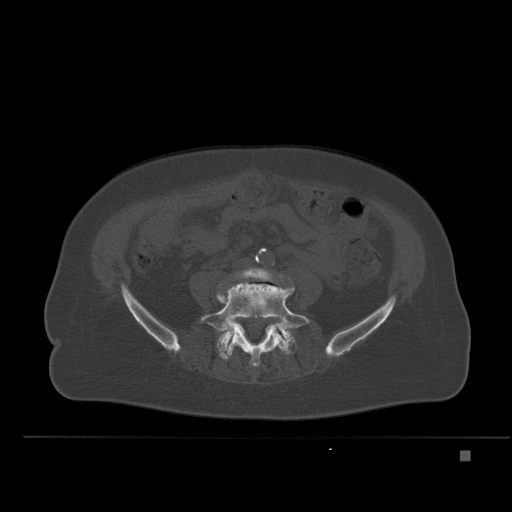
CT including the spine, one axial slice. Position 163 of 477 along the scan axis. Bone window (W 1800 / L 400 HU). 512 × 512 image matrix, field of view 422 × 422 mm. Female patient, age 74 years. Case-level facts recorded for this patient, not image findings: primary cancer: colon.
Structures marked on this image (semi-automatically segmented with operator editing):
- L4 vertebra: bounding box (x1, y1, x2, y2) in pixels: (218, 267, 283, 296)
- L5 vertebra: (199, 278, 310, 367)